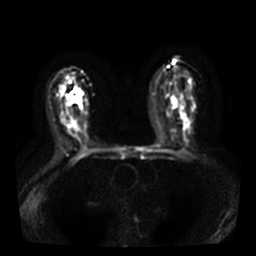
Breast MRI, one axial slice. Slice 19 of 36 in the series (ordered by position). Diffusion-weighted series; image 2 of 4 stored at this slice position (different b-values; order by instance number). 3 T. 256 × 256 image matrix, field of view 320 × 320 mm. Female patient.
Structures marked on this image (manually delineated by an expert):
- tumour on diffusion-weighted imaging: bounding box [x1, y1, x2, y2] px = [70, 90, 82, 104]